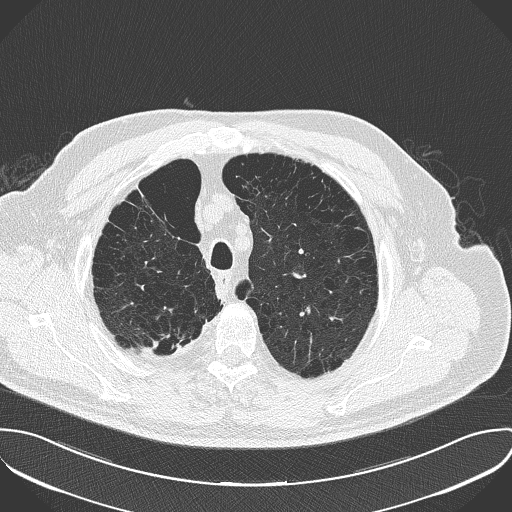
Low-dose screening chest CT, axial slice. First (baseline) screen. Lung window (W 1500 / L -600 HU). 2 mm slice thickness. Lung (sharp) reconstruction kernel (B50f). Male participant, aged 68 years at enrolment. Current smoker at enrolment.
- Expert-annotated lung lesion, box from (x=125, y=323) to (x=197, y=368) px.
- The screening reader recorded 3 non-calcified nodules or masses ≥4 mm on this exam (left lower lobe, left upper lobe, right lower lobe); which of them this box marks is not recorded.
- Official screen result: positive, change unspecified: nodule(s) >= 4 mm or enlarging nodule(s), mass(es), or other non-specific abnormalities suspicious for lung cancer.
- Lung cancer was diagnosed 661 days after this screen (after the second annual screen): adenocarcinoma, NOS, right upper lobe, stage IV (AJCC 6th edition), 29 mm at pathology.